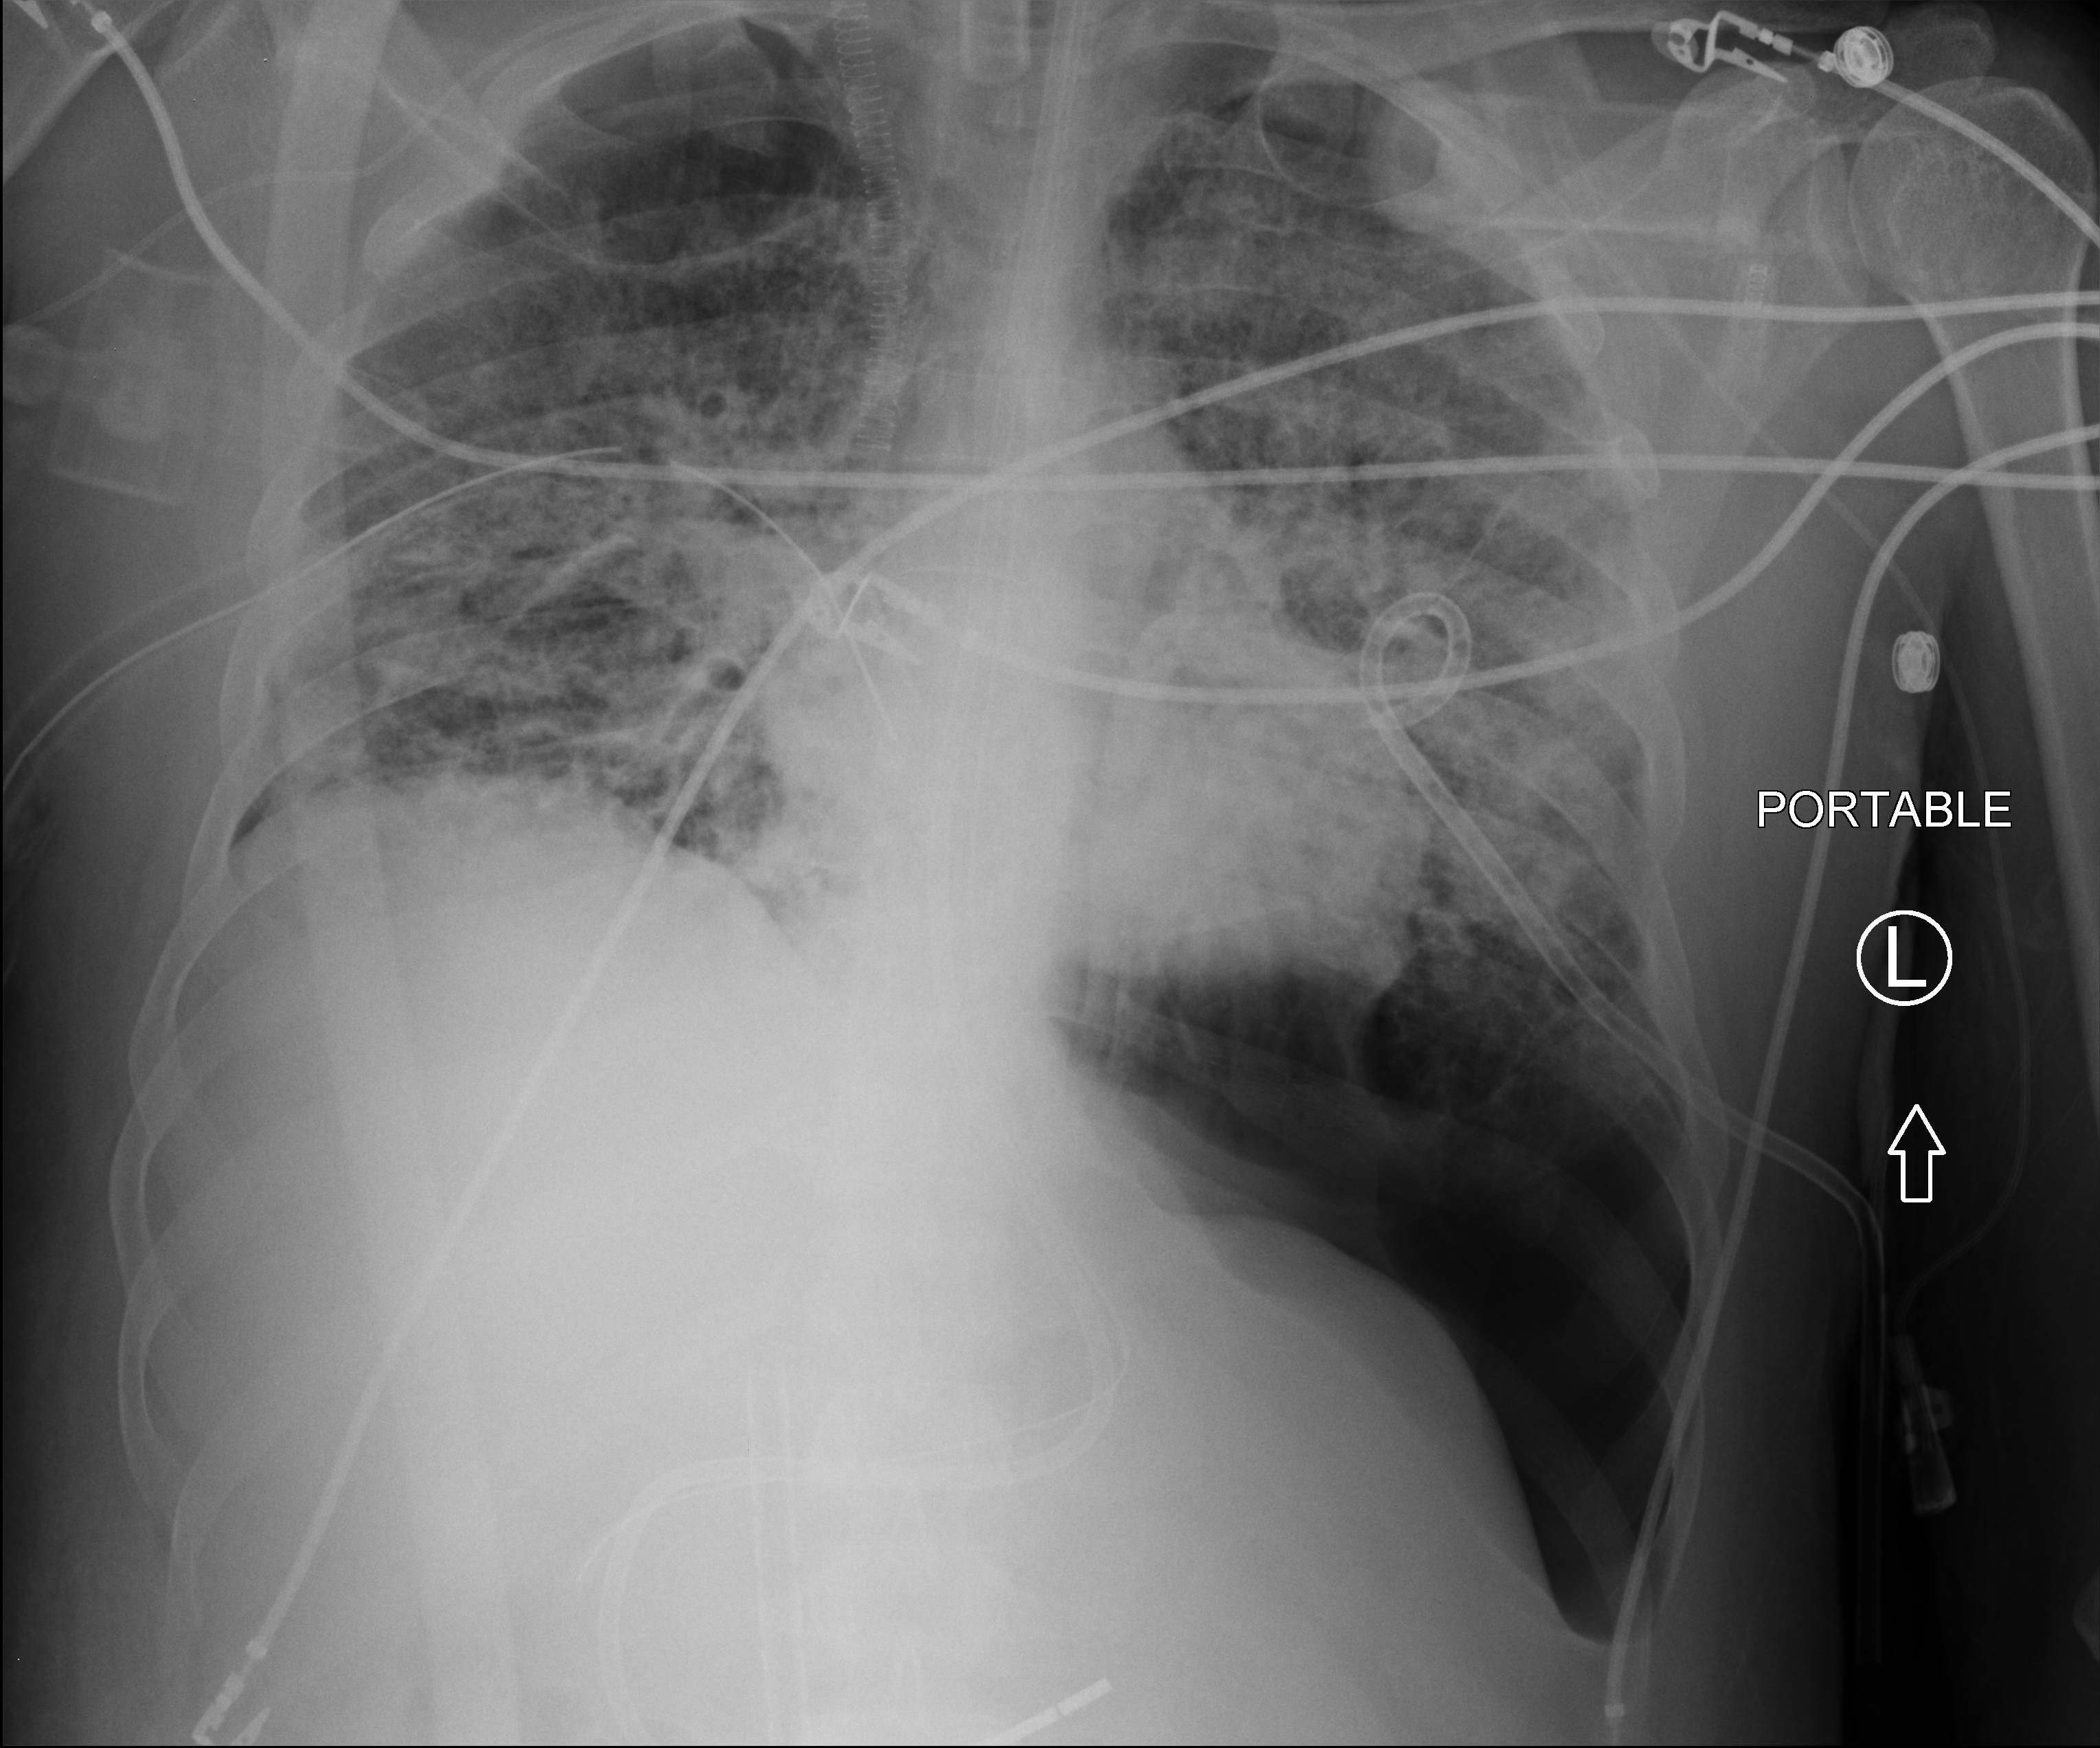
Chest X-ray (portable); anteroposterior (AP) projection. Adult patient hospitalised with COVID-19, age 18–59 years.
From the hospital-stay record, not from the radiograph (when in the stay this image was taken is not recorded):
- length of hospital stay: 60 days
- mechanically ventilated during this hospital stay: yes